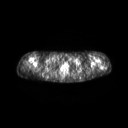
FDG PET of an extremity soft-tissue mass (from a PET/CT study), one axial slice. Position 213 of 267 along the scan axis. 3.27 mm slice thickness. 128 × 128 image matrix, field of view 600 × 600 mm. Female patient, age 28 years. From the clinical record (not read from this slice): histological type: malignant fibrous histiocytoma; grade: low; site of the primary tumour: left arm.
Annotated regions visible in this slice (expert contour drawn on MRI and transferred to this co-registered scan by the dataset authors):
- gross tumour volume (mass): box from (x=99, y=66) to (x=104, y=69) px